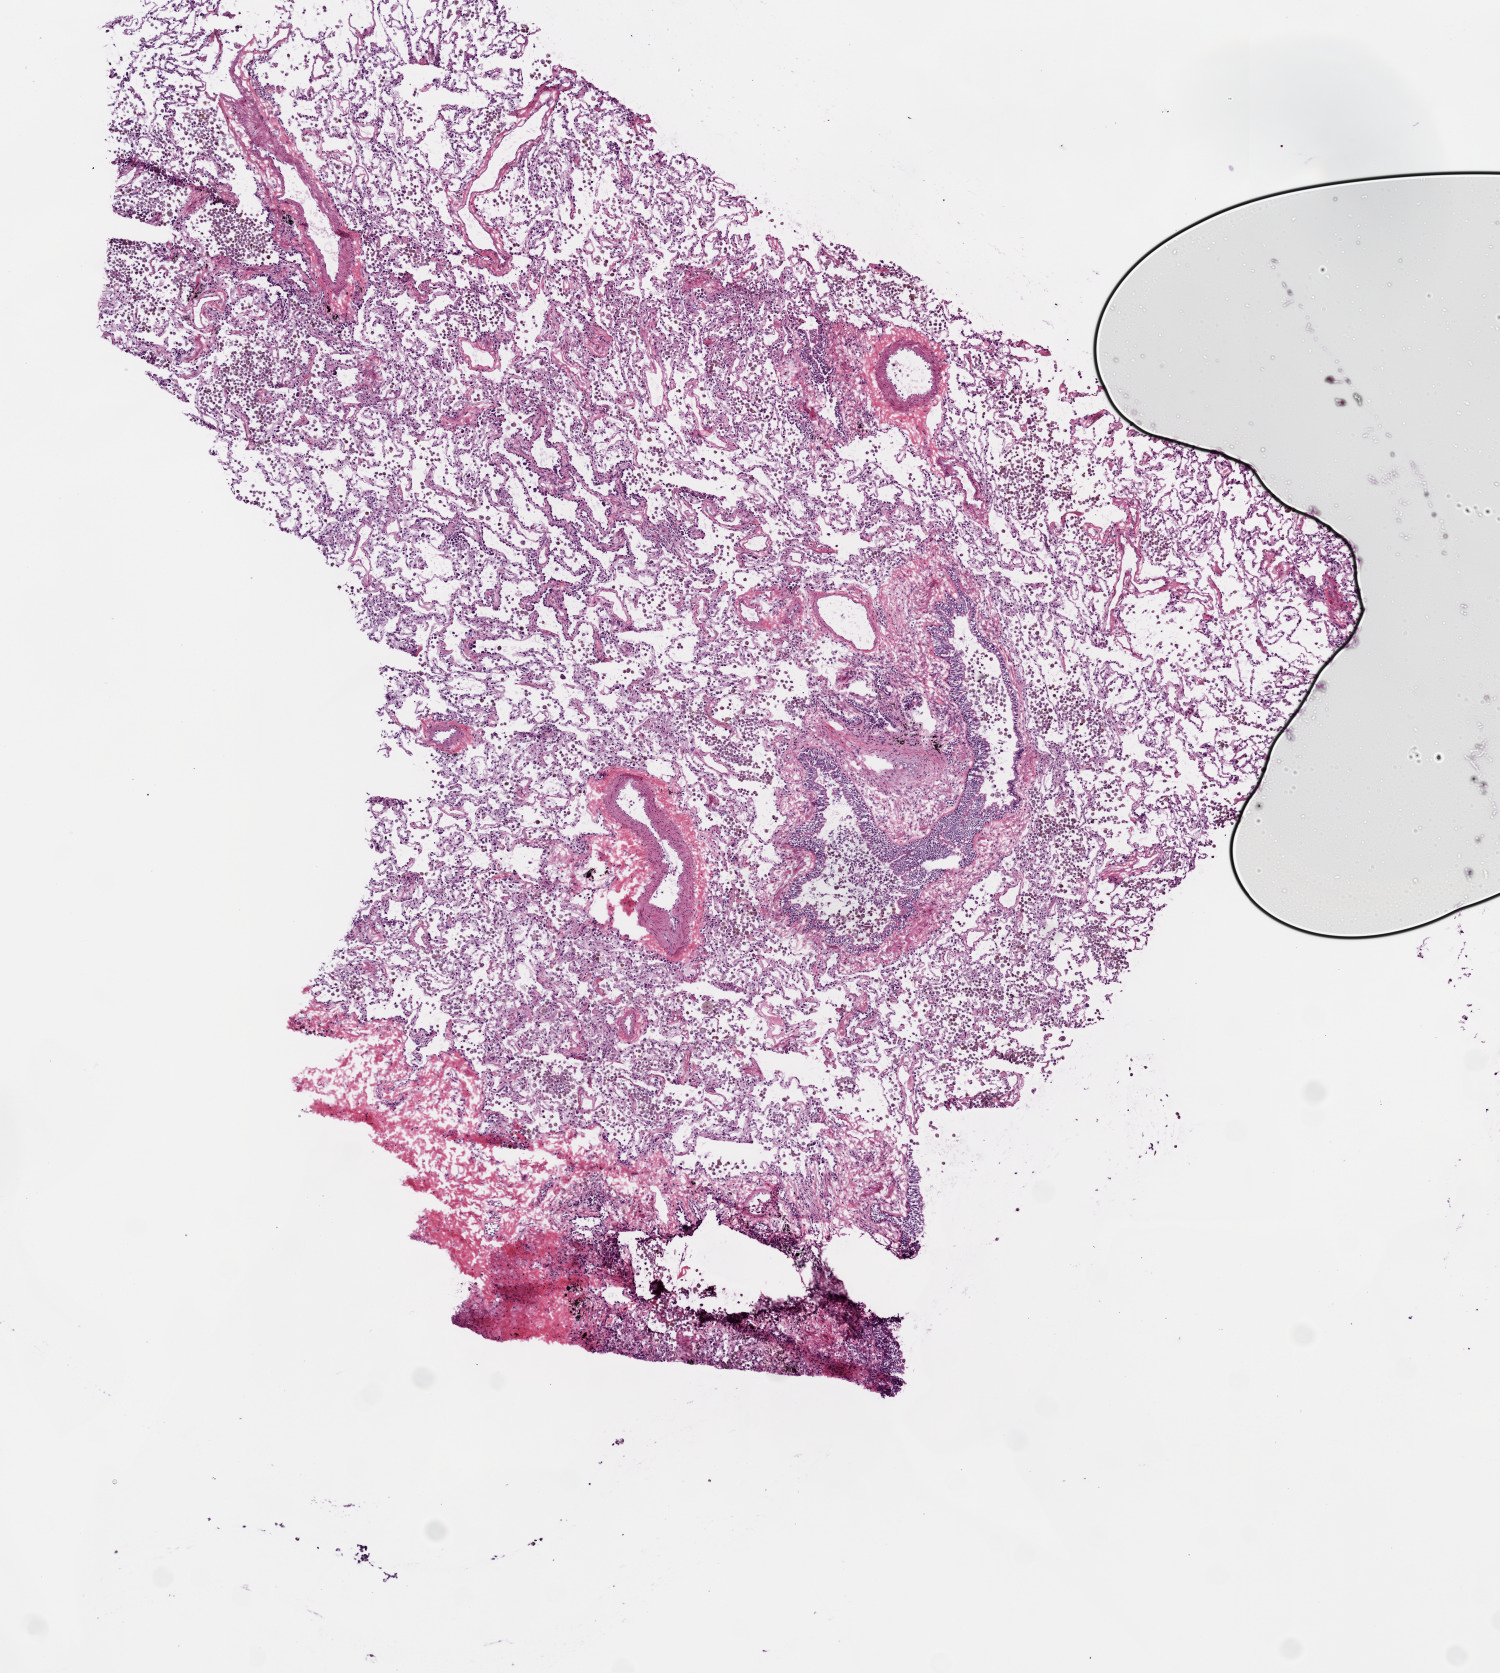
Hematoxylin and eosin (H&E) stained whole-slide image, whole scanned area (about 6.0 x 6.7 mm) shown as a low-resolution overview; frozen section; solid tissue normal (non-tumour tissue) sample from the lung. Female patient; age at initial diagnosis 57 years.
This section: solid tissue normal sample (biorepository sample class). Patient diagnosis: Adenocarcinoma, NOS (upper lobe, lung).